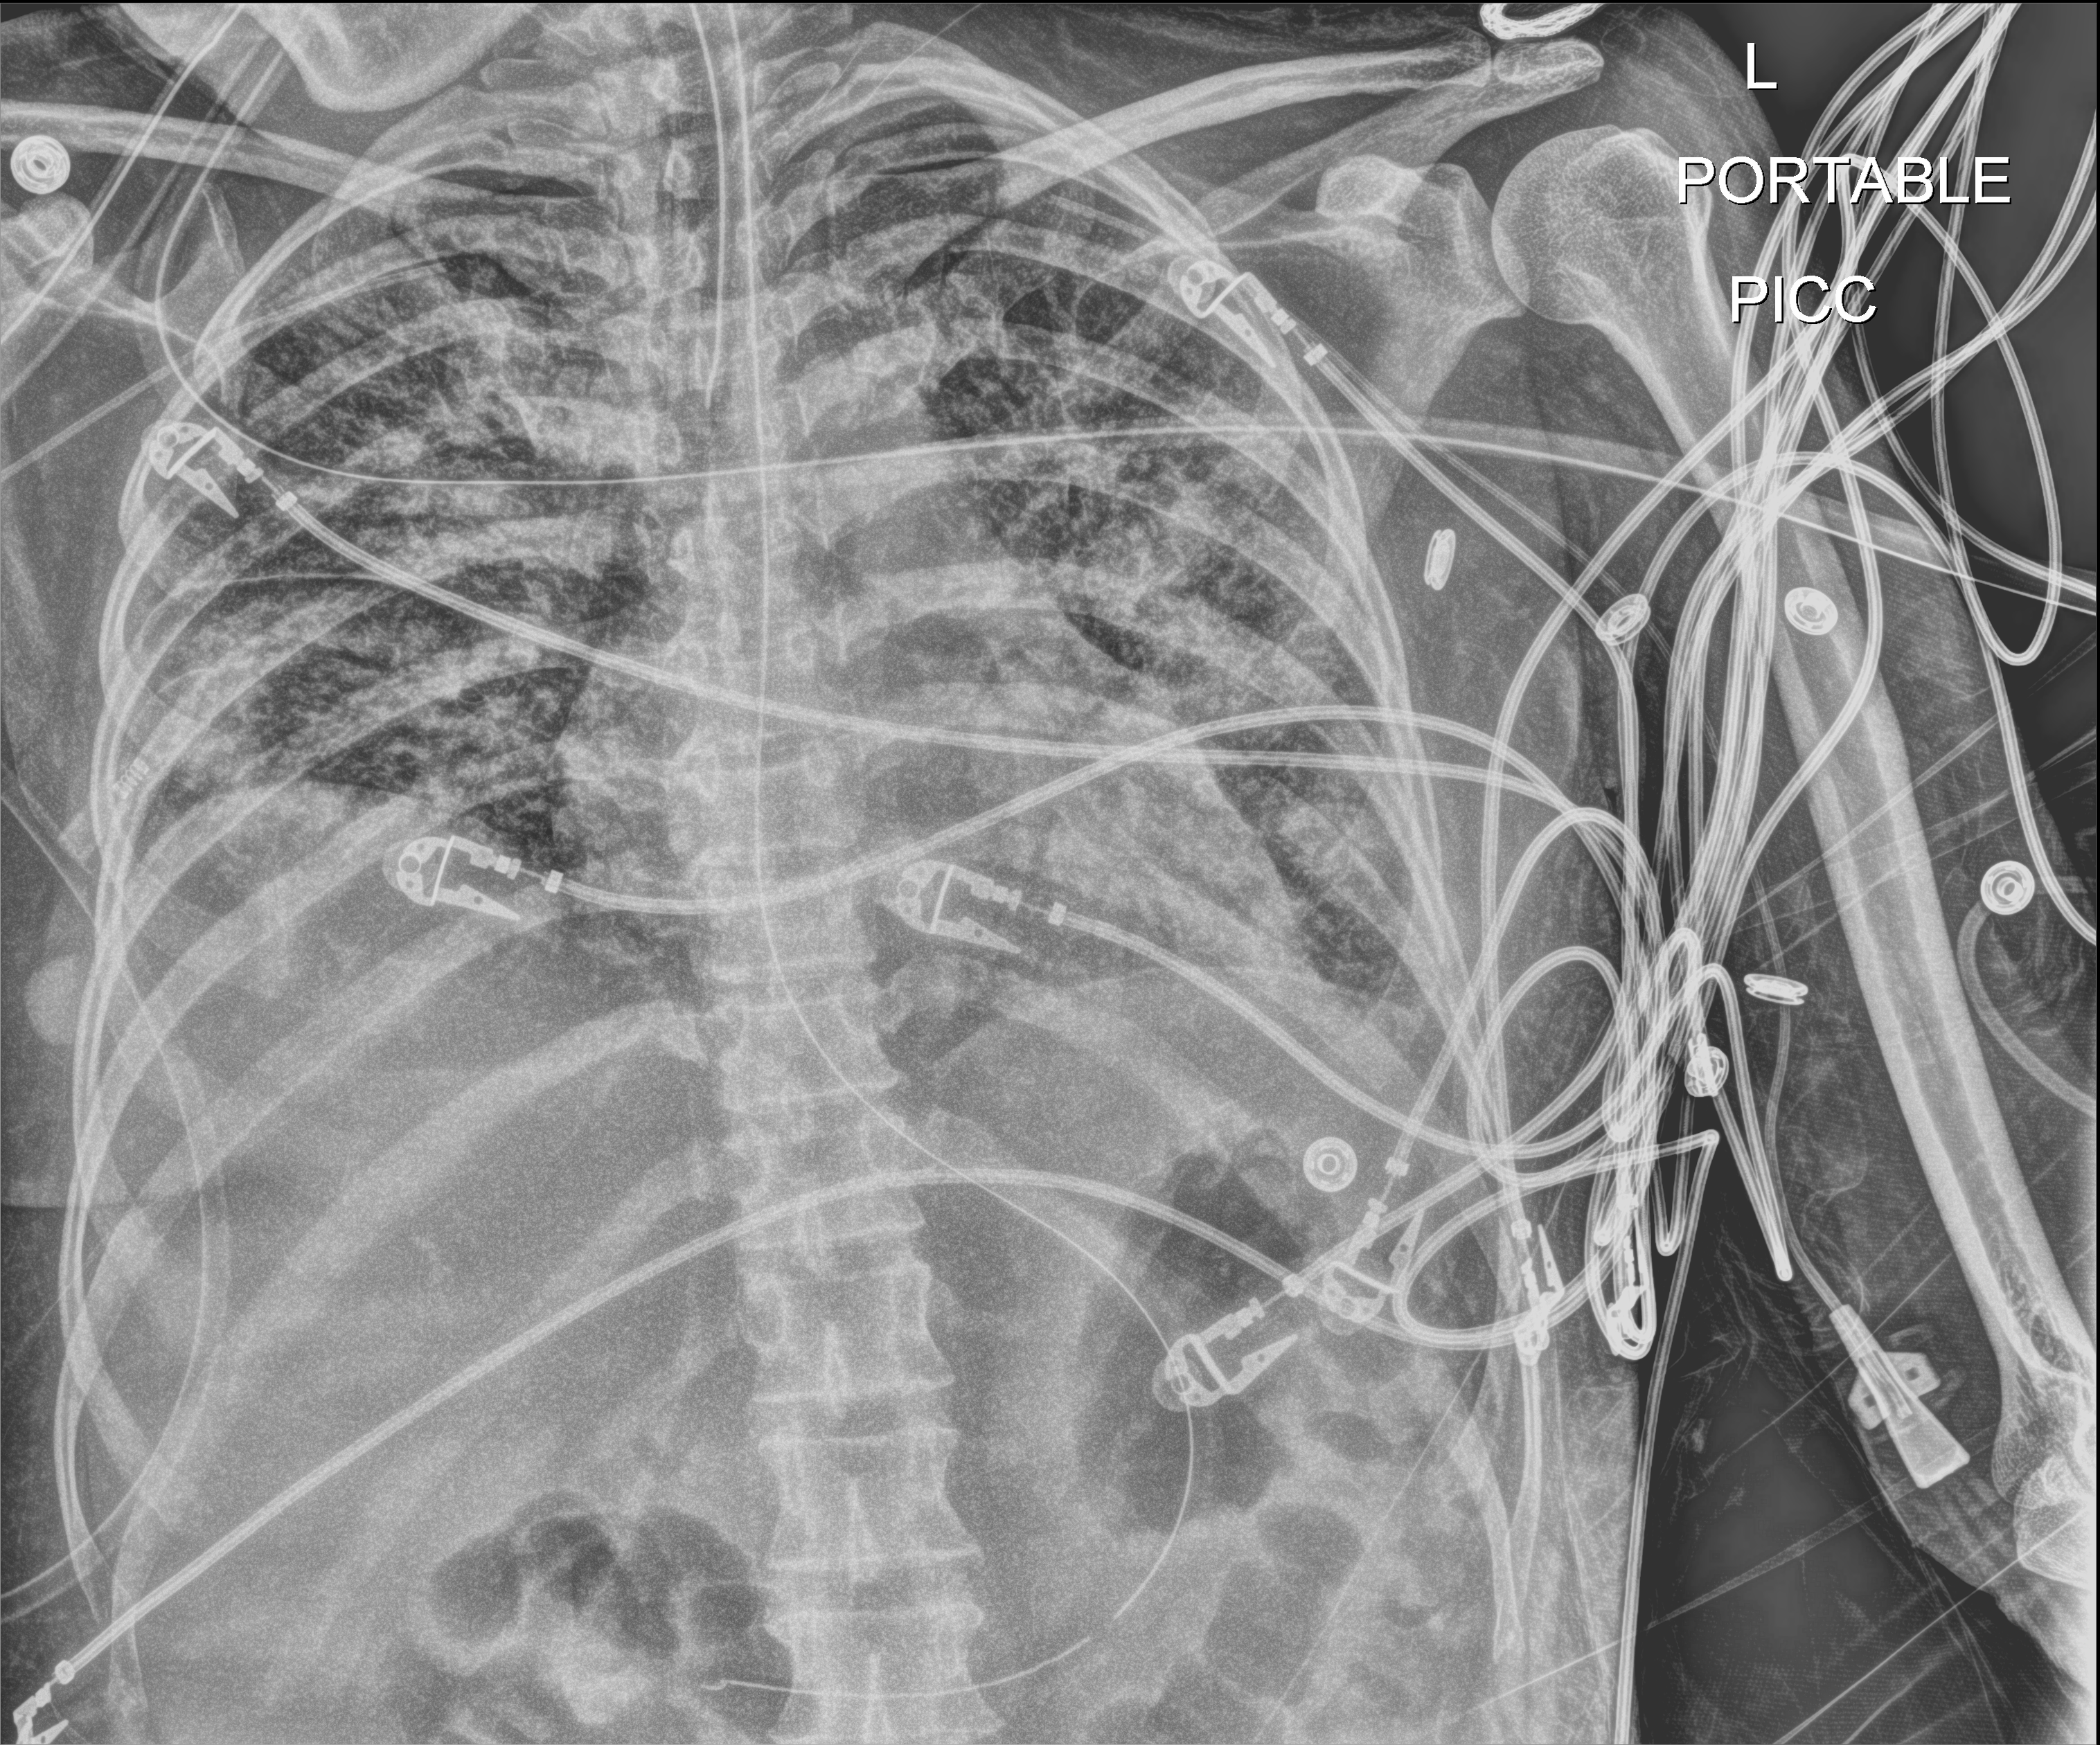
Portable chest radiograph; anteroposterior (AP) projection. Patient hospitalised with COVID-19; female, aged 18–59 years.
Hospital-stay facts (about this admission, not read from this image; timing relative to this image not recorded):
- hypertension (admission record): no